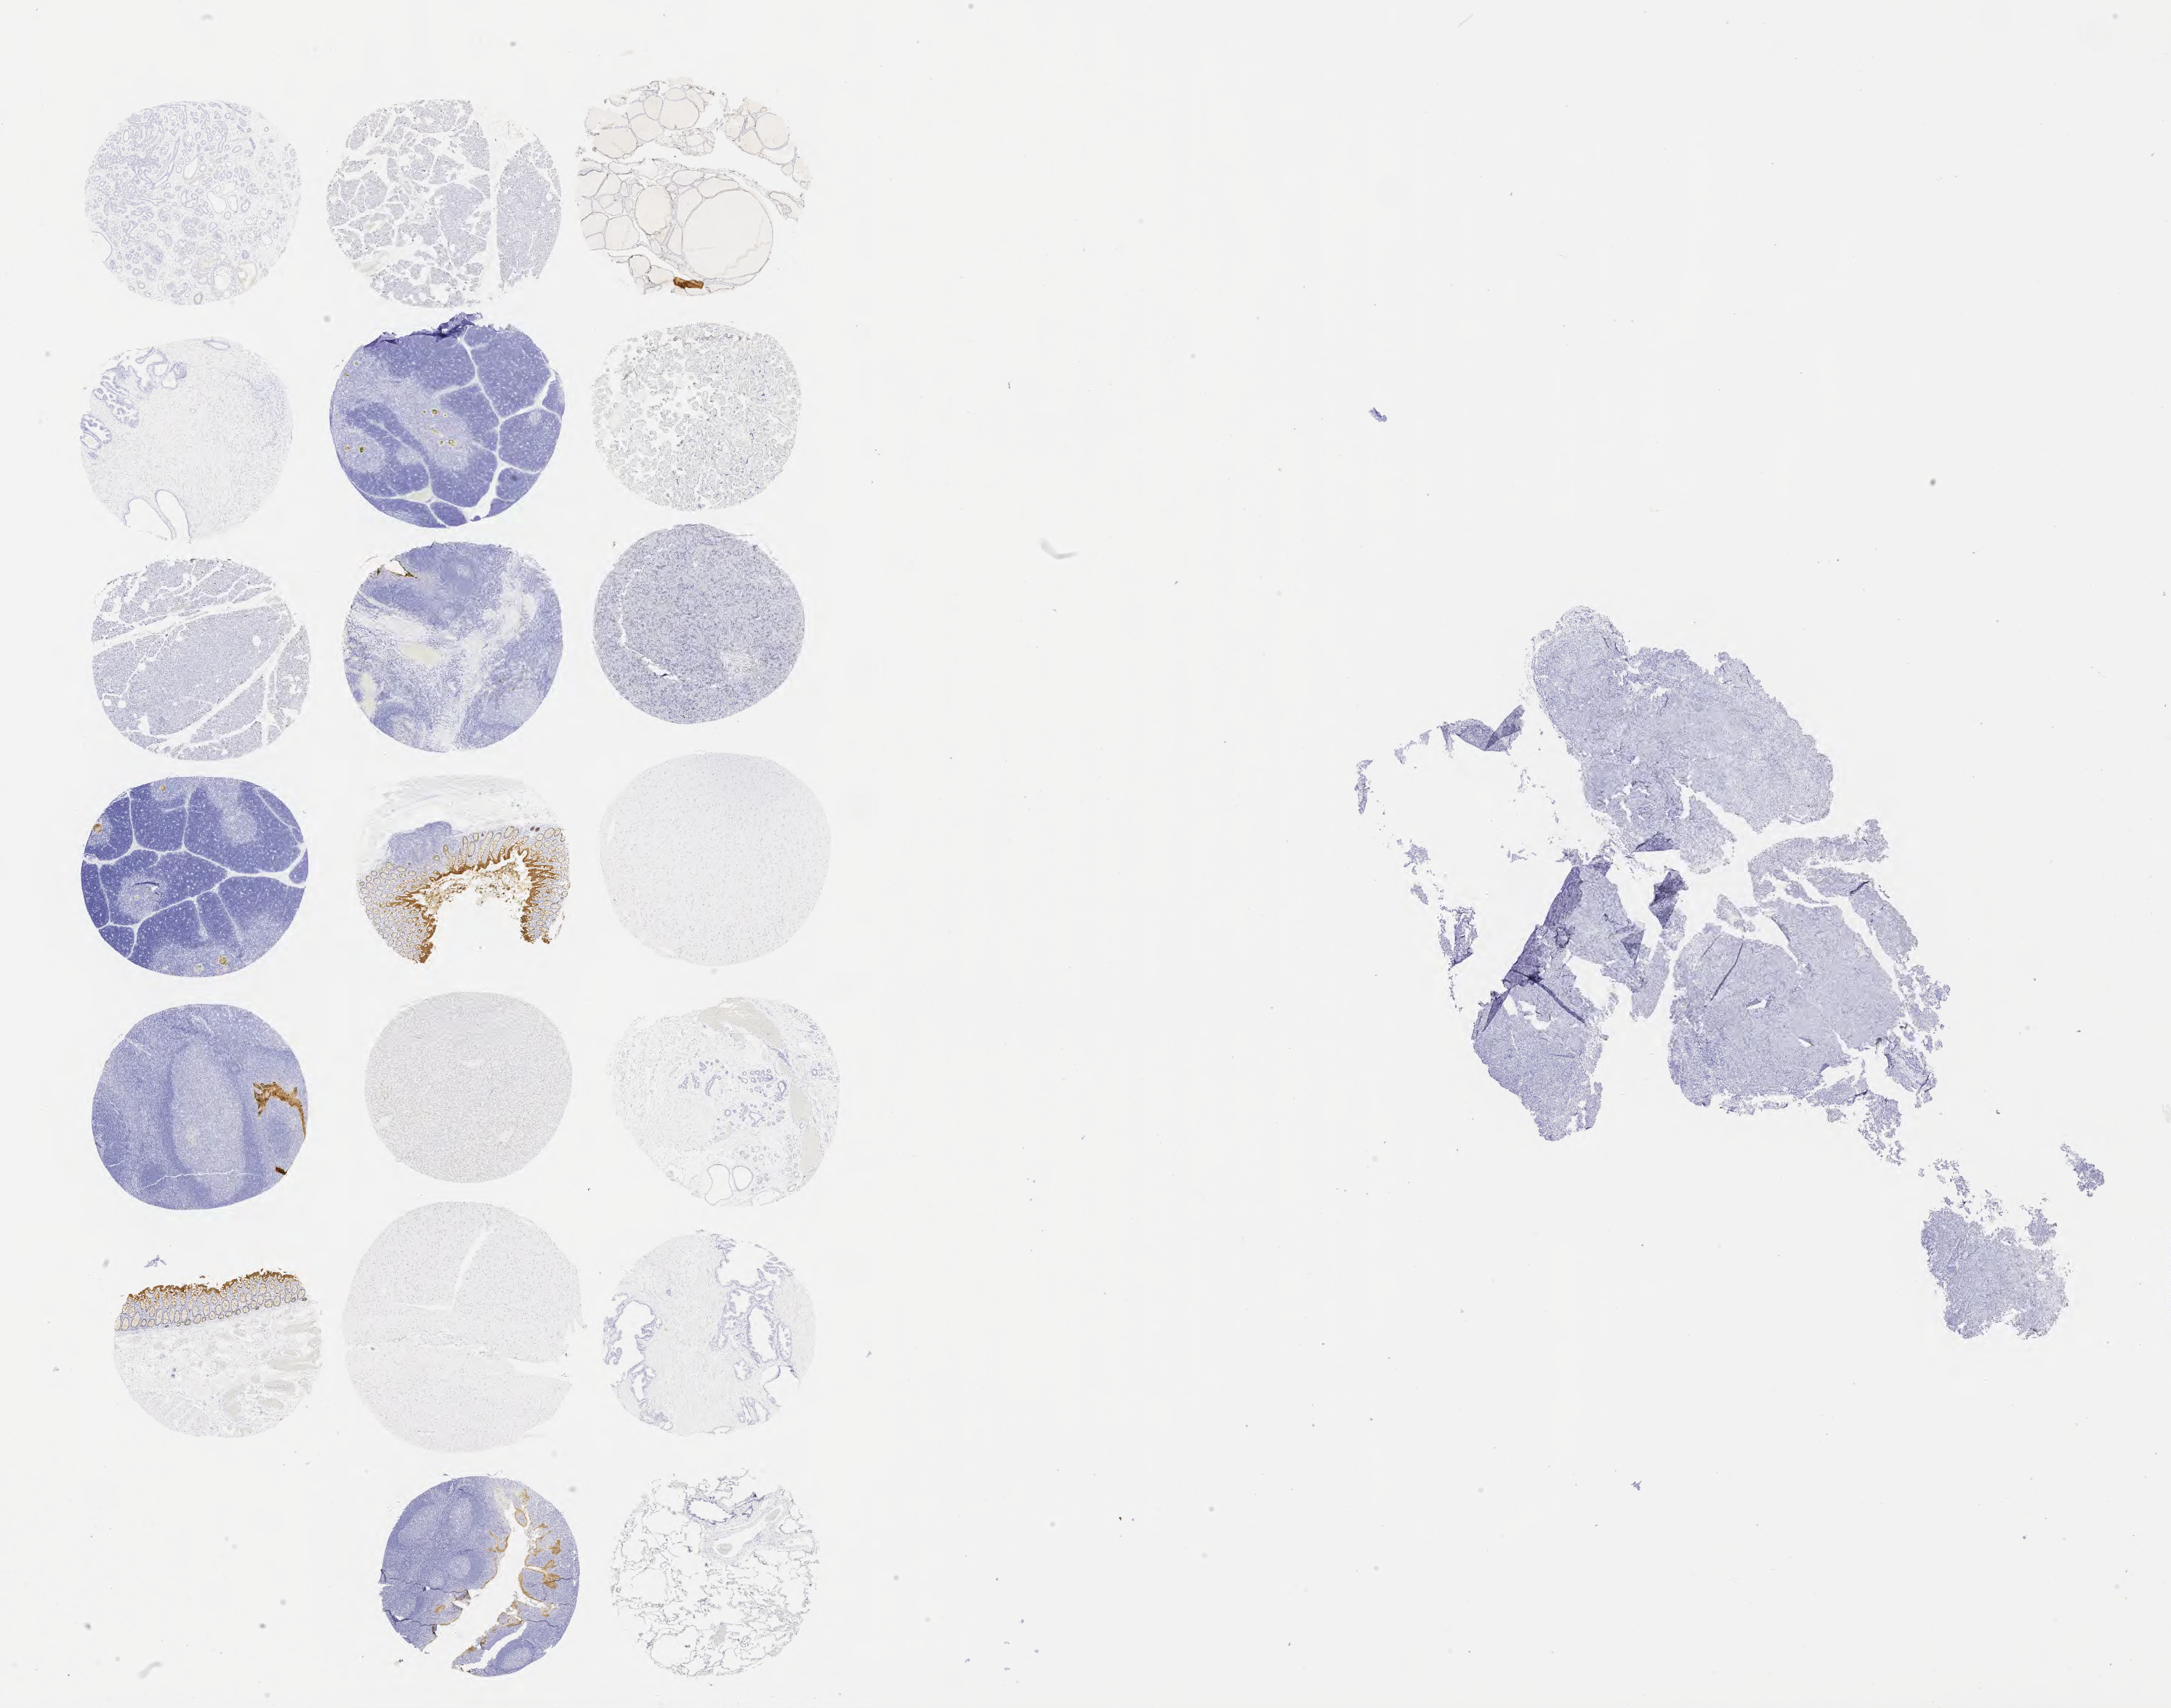
IHC for carcinoembryonic antigen (CEA), whole-slide image — a low-resolution overview of the entire scanned area, about 24.2 x 19.0 mm, specimen: tumor tissue, anatomic site: cervix. Patient female; aged 75.
Histologic diagnosis: Adenocarcinoma, NOS.